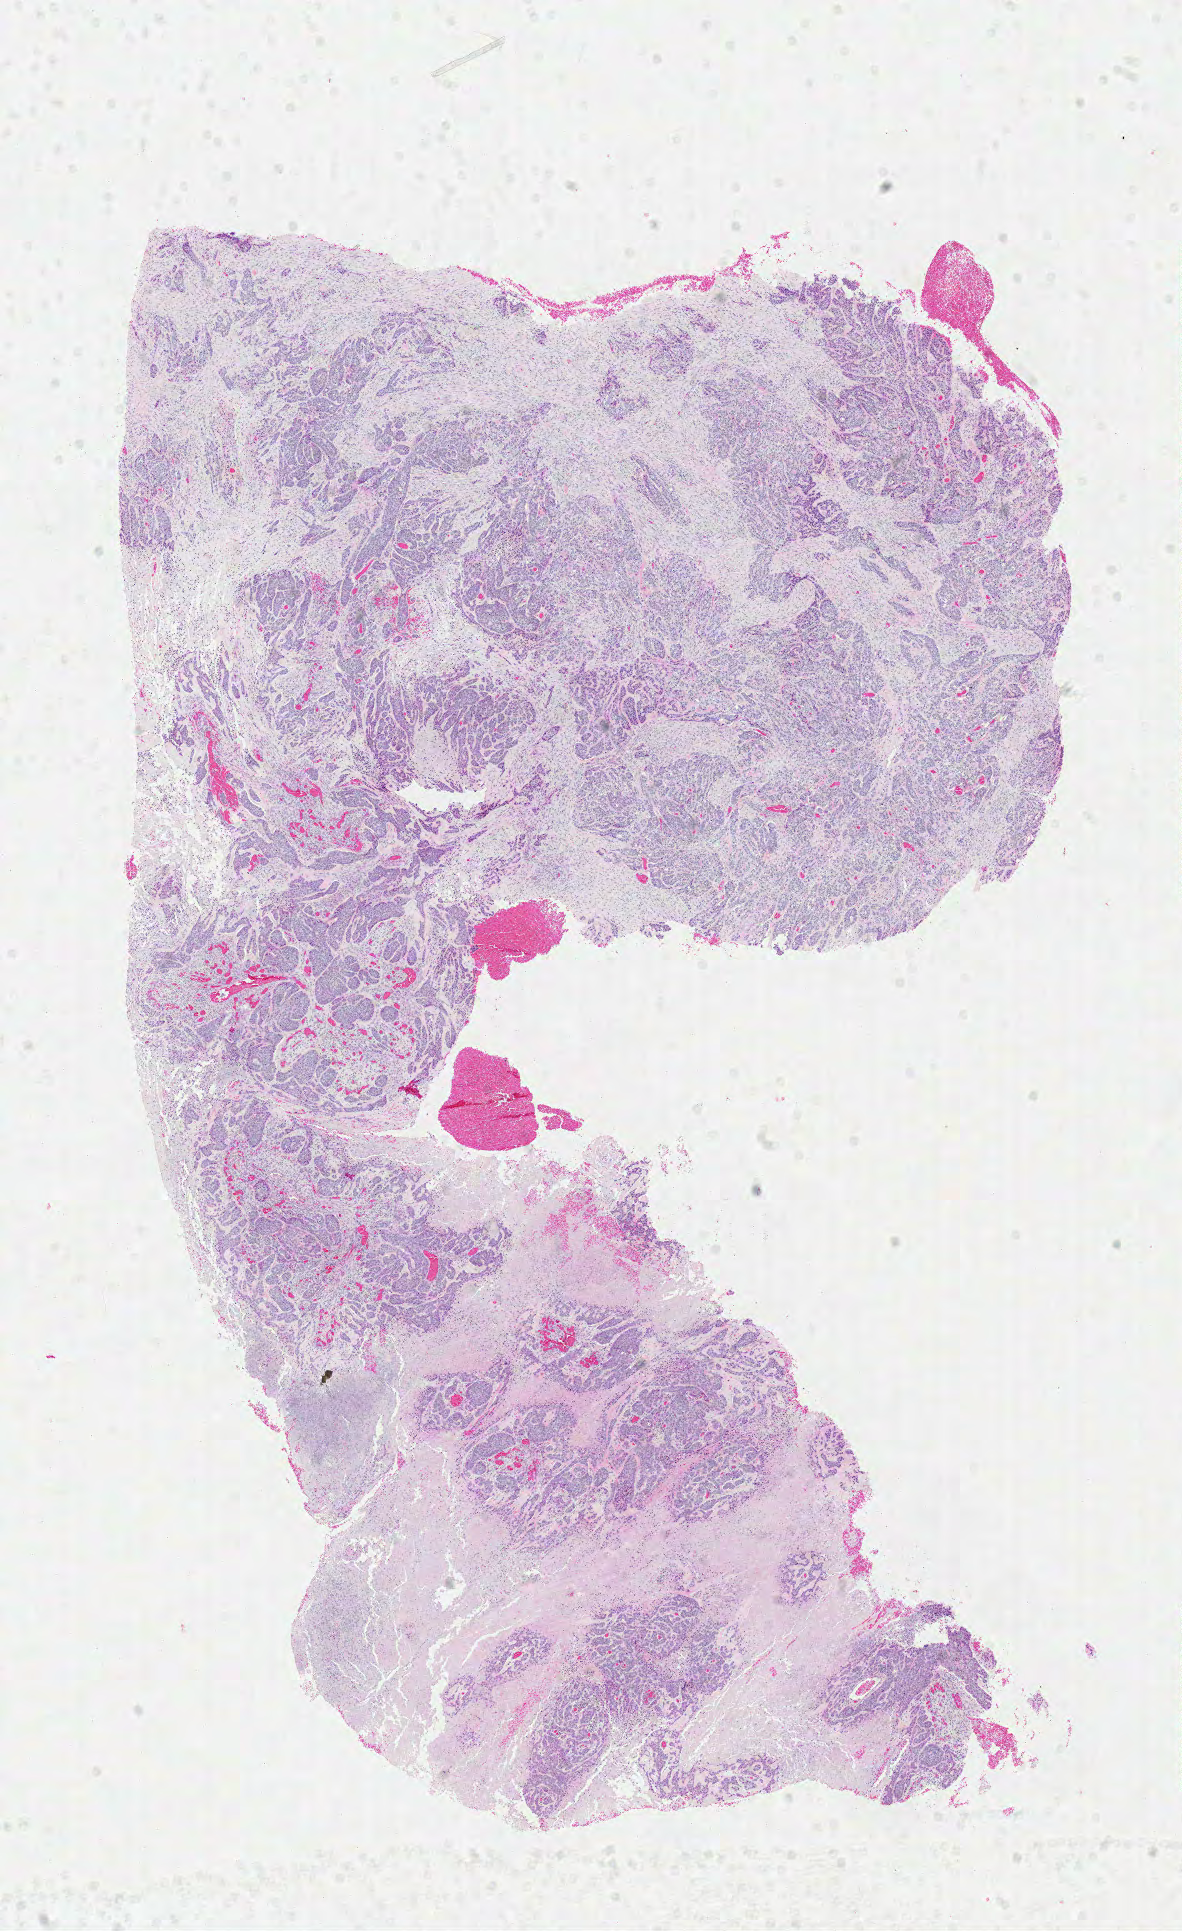
Digitized H&E tissue section (whole slide), shown as a low-resolution overview of the whole scanned area (about 9.3 x 15.2 mm); FFPE section; lung, primary tumour sample. Male, age 75 years at initial diagnosis.
Pathologic diagnosis: Squamous cell carcinoma, NOS (upper lobe, lung). TNM: T4 N0 M0. AJCC pathologic stage: IIIB (6th edition).